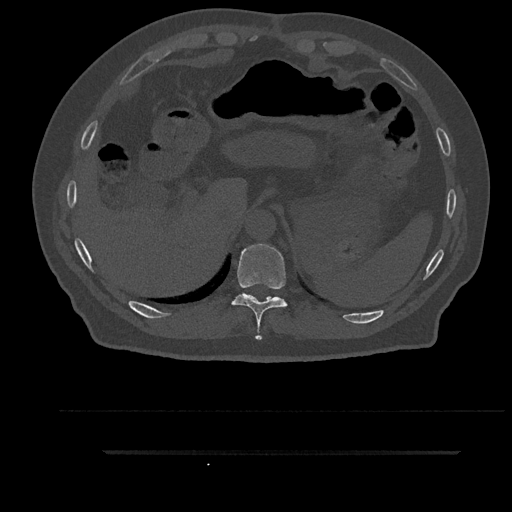
CT including the spine, one axial slice. Position 358 of 797 along the scan axis. Reconstruction kernel Br40s/3. Bone window (W 1800 / L 400 HU). 0.5 mm slice thickness. 512 × 512 image matrix. Male patient, age 63 years. Case-level facts recorded for this patient, not image findings: primary cancer: renal.
Outlined on this slice (semi-automatically segmented with operator editing):
- T10 vertebra: bounding box [x1, y1, x2, y2] px = [232, 244, 287, 340]
- T11 vertebra: [246, 294, 271, 297]